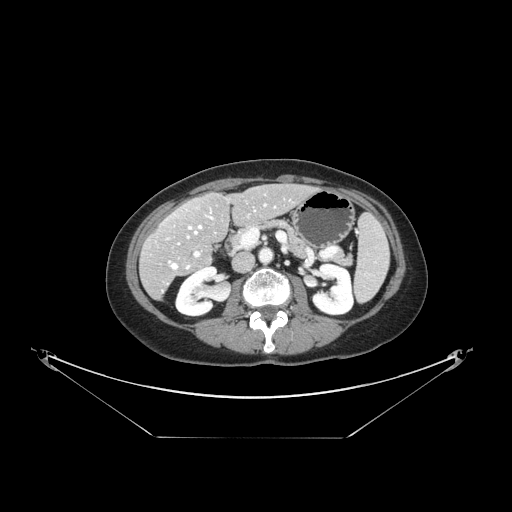
Contrast-enhanced abdominal CT, one axial slice; slice 66 of 148 in the series (ordered by position); reconstruction kernel STANDARD; 120 kVp; intravenous contrast given; soft-tissue window (W 400 / L 40 HU); 512 × 512 image matrix, field of view 500 × 500 mm. Female patient, age 73 years. From the clinical record (not read from this slice): diagnosis: colorectal cancer liver metastases, imaged before liver resection; multiple liver metastases: no; largest metastasis: 1 cm; disease in both lobes: no.
Structures marked on this image (manually delineated by an expert):
- hepatic veins: bounding box <169,211,212,269> (left, top, right, bottom; pixels)
- liver: <142,184,313,298>
- planned liver remnant (the part of the liver to remain after resection): <167,185,312,249>
- portal vein (with intrahepatic branches): <195,252,199,256>